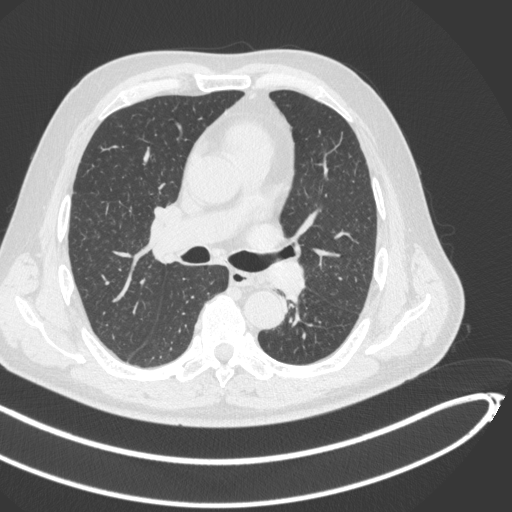
Chest CT, one axial slice. Position 272 of 466 along the scan axis. Reconstruction kernel B31f. 120 kVp. Lung window (W 1500 / L -600 HU). 1 mm slice thickness. 512 × 512 image matrix. Patient: male, 64 years. From the clinical record (not read from this slice): clinical TNM (as recorded): T1c N0 M0; histopathological grade: G2.
Annotated regions visible in this slice (rectangle marked by the reading radiologist):
- lung tumour (recorded histology: squamous cell carcinoma): bounding box (x1, y1, x2, y2) in pixels: (273, 263, 310, 303)